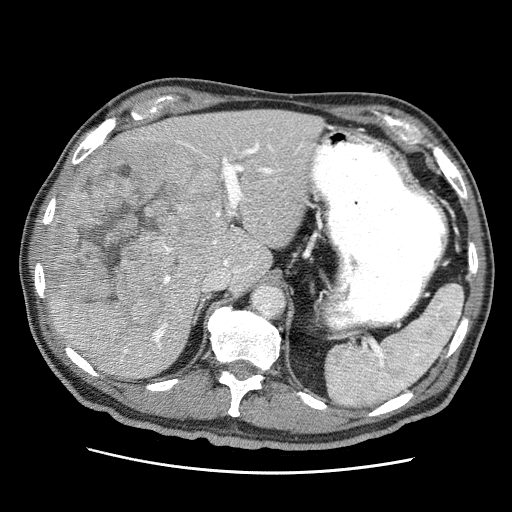
Contrast-enhanced abdominal CT (liver protocol), one axial slice. Position 37 of 75 along the scan axis. Reconstruction kernel STANDARD. 120 kVp. Soft-tissue window (W 400 / L 40 HU). 512 × 512 image matrix, field of view 360 × 360 mm. Case-level facts recorded for this patient, not image findings: diagnosis: hepatocellular carcinoma (patient treated with transarterial chemoembolisation; whether this scan precedes or follows treatment is not stated here); TNM stage (as recorded): Stage-IIIA; Child-Pugh class: A; tumour differentiation: well differentiated; tumour nodularity: multinodular.
Annotated regions visible in this slice (semi-automatic segmentation, software-assisted and operator-edited):
- liver parenchyma outside the tumour (the mass and vessels are separate outlines, so this box may not span the whole liver): bounding box (x1, y1, x2, y2) in pixels: (44, 110, 324, 378)
- mass: (48, 134, 222, 341)
- liver vessels: (53, 140, 302, 364)